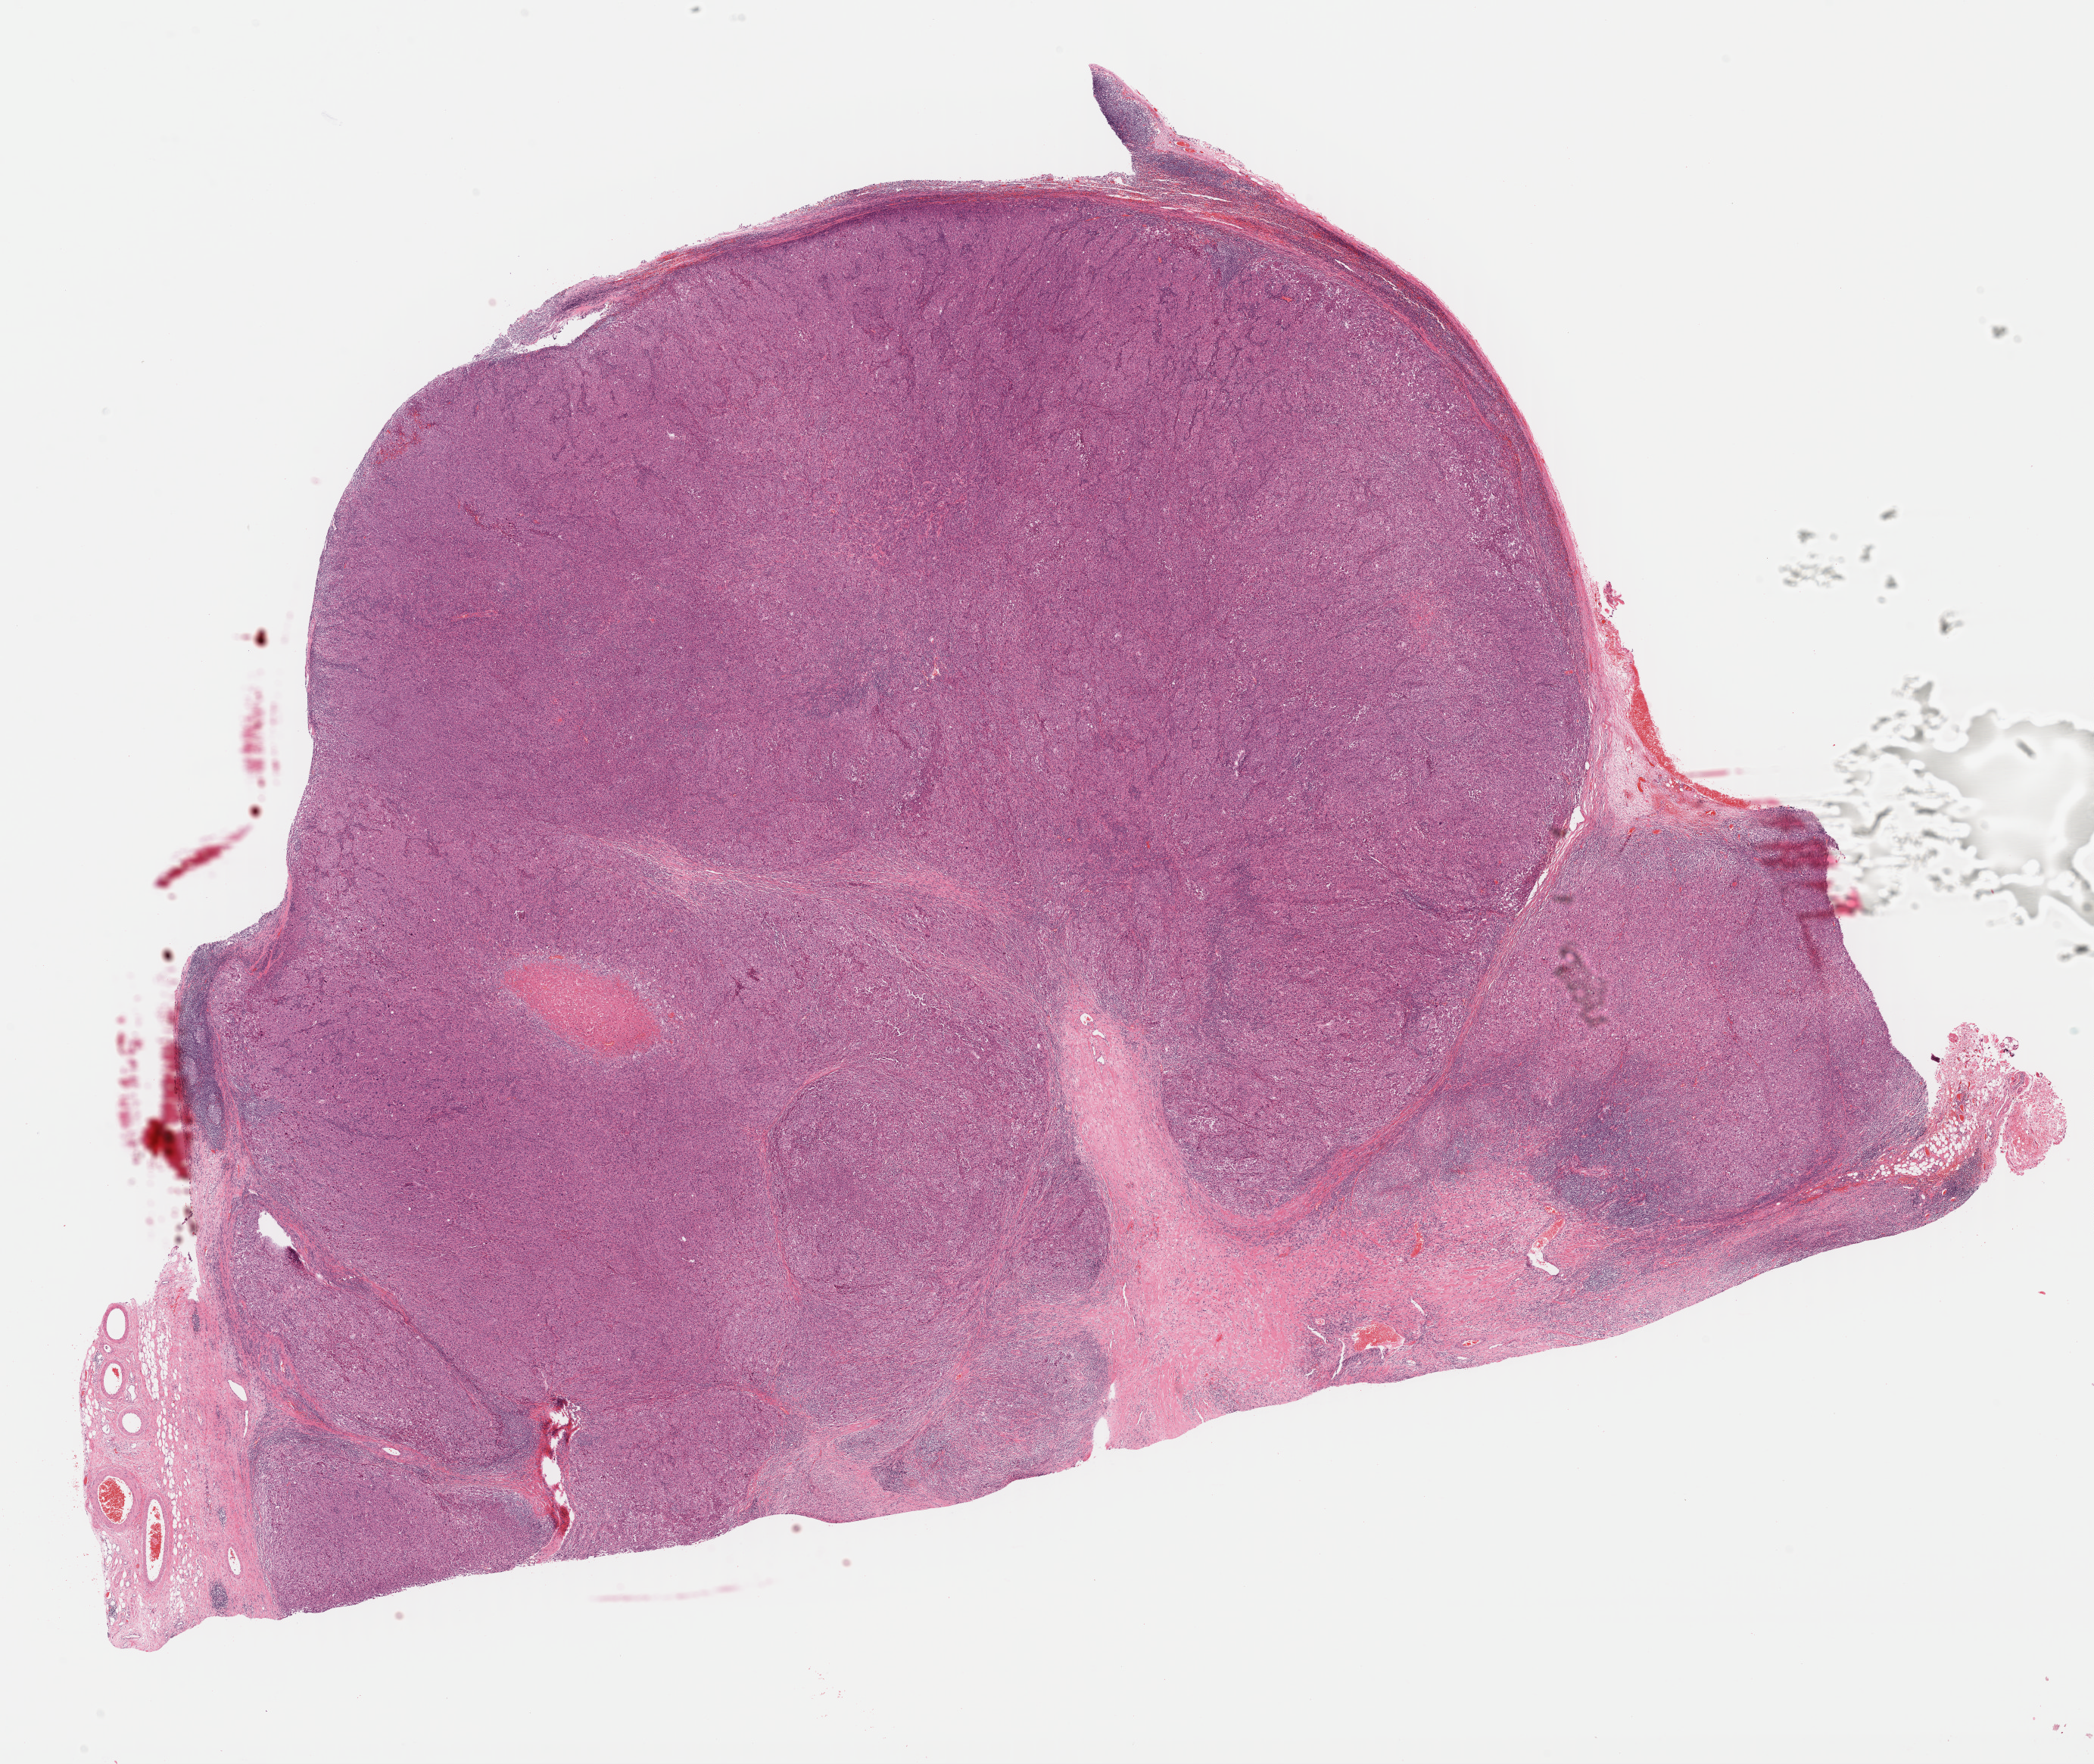
Hematoxylin and eosin (H&E) stained whole-slide image — a low-resolution overview of the entire scanned area, about 21.7 x 18.3 mm (slide scanned at 40x), formalin-fixed paraffin-embedded (FFPE) diagnostic section, metastatic tumour sample, sampled site: lymph nodes of axilla or arm. Female, age 57 years at initial diagnosis.
This section: metastatic tumour tissue. Patient diagnosis: Malignant melanoma, NOS.